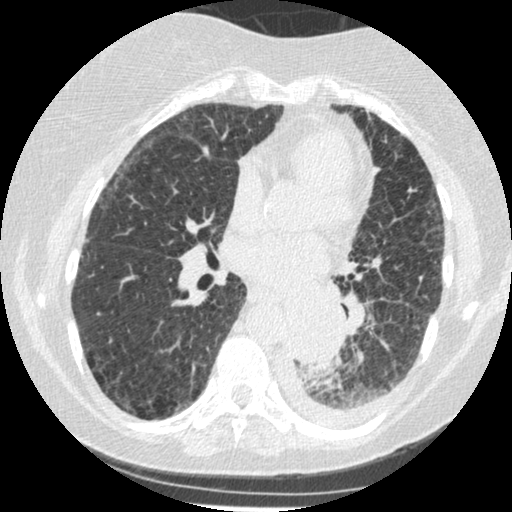
Low-dose screening chest CT, one axial slice. Slice 115 of 341 in the series (ordered by position). Reconstruction kernel STANDARD. Lung window (W 1500 / L -600 HU). 1.25 mm slice thickness. 512 × 512 image matrix, field of view 310 × 310 mm.
Annotated regions visible in this slice (expert manual segmentation):
- lesion 1 (tumor, lower lobe of left lung): bounding box [x1, y1, x2, y2] px = [284, 302, 343, 365]